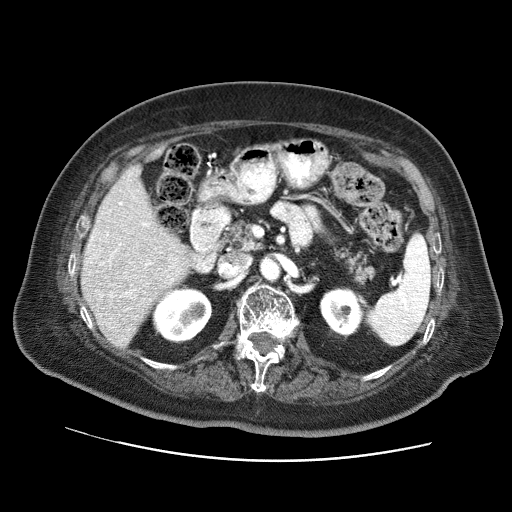
Contrast-enhanced abdominal CT (liver protocol), one axial slice. Position 31 of 73 along the scan axis. Reconstruction kernel STANDARD. 120 kVp. Soft-tissue window (W 400 / L 40 HU). 2.5 mm slice thickness. 512 × 512 image matrix, field of view 380 × 380 mm. From the clinical record (not read from this slice): diagnosis: hepatocellular carcinoma (patient treated with transarterial chemoembolisation; whether this scan precedes or follows treatment is not stated here); TNM stage (as recorded): Stage-I; Child-Pugh class: A; tumour nodularity: uninodular.
Structures marked on this image (semi-automatic segmentation, software-assisted and operator-edited):
- liver parenchyma outside the tumour (the mass and vessels are separate outlines, so this box may not span the whole liver): bounding box <82,165,188,348> (left, top, right, bottom; pixels)
- liver vessels: <87,202,175,298>